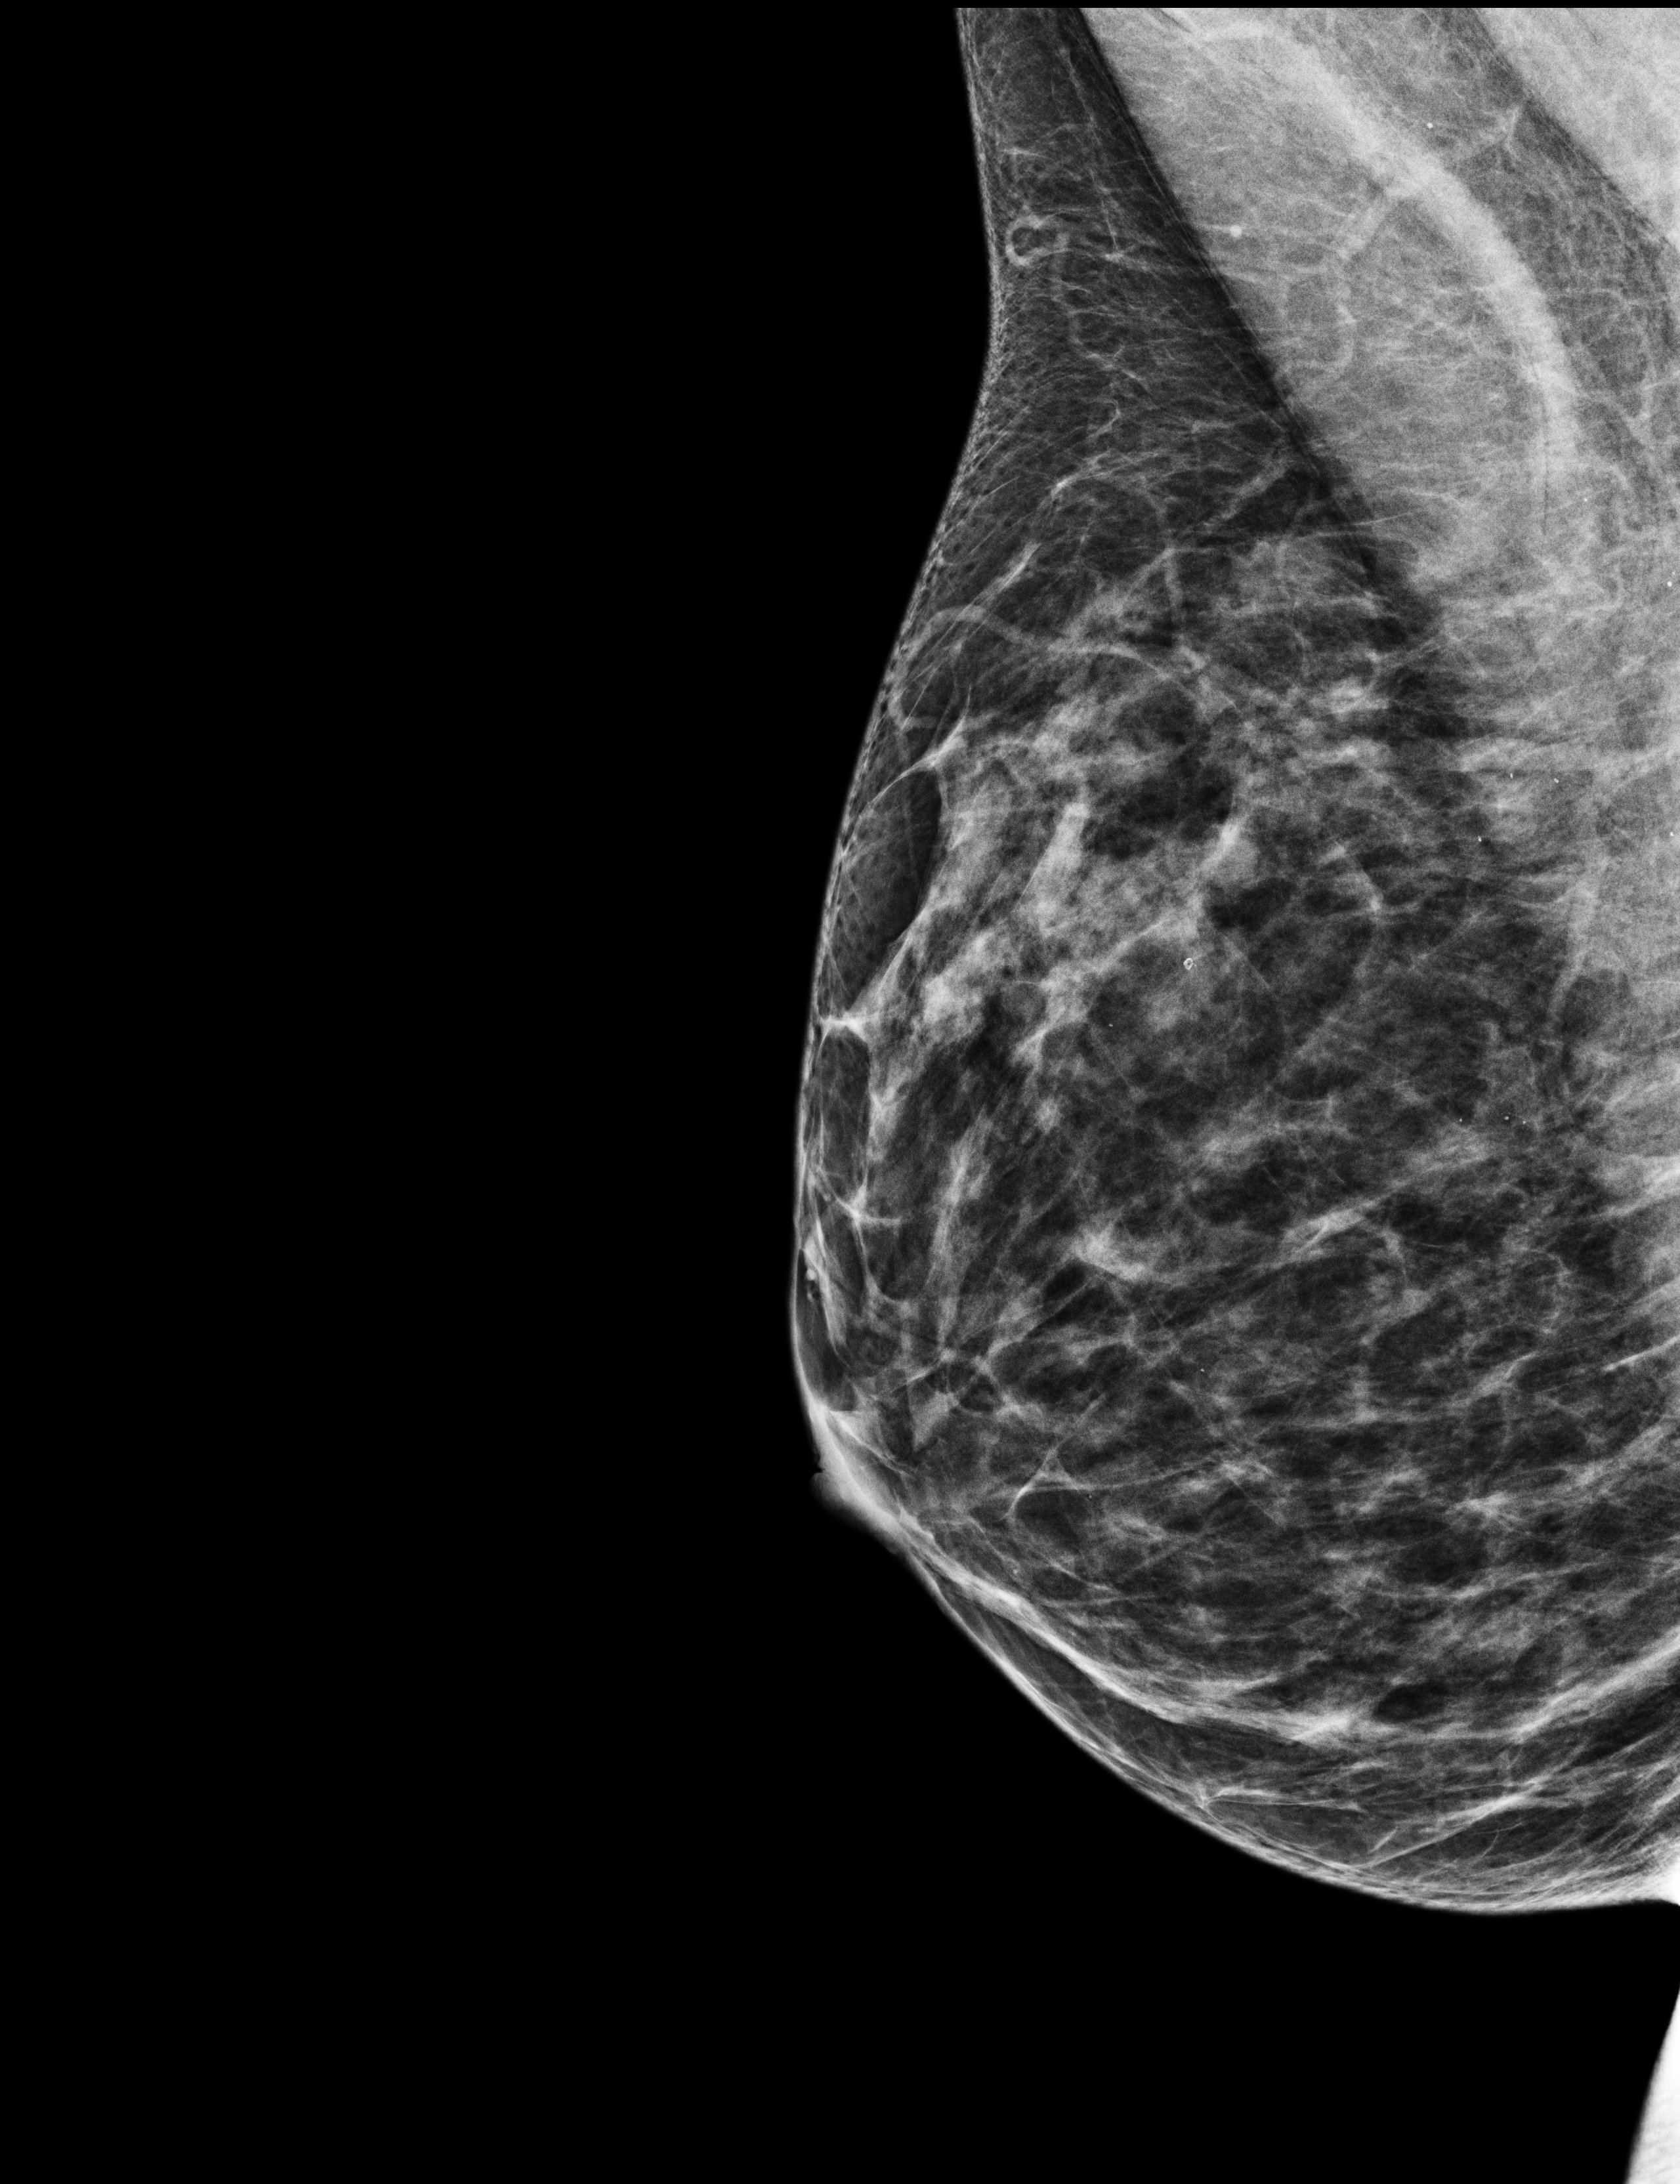
Screening examination, system: Selenia Dimensions. Patient: female, 44 years.
Image type: full-field digital mammogram. Breast: right. Projection: medio-lateral oblique projection.